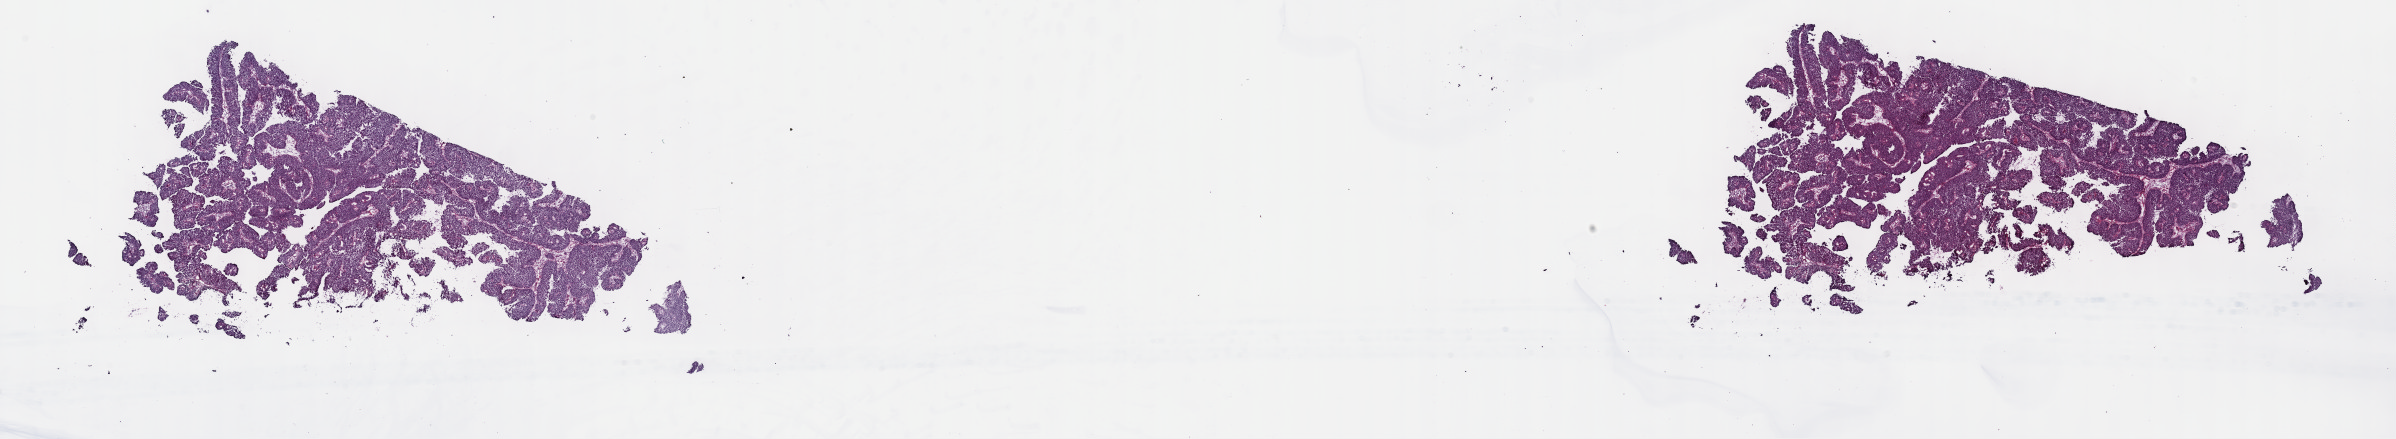
H&E-stained whole-slide image — whole scanned area (about 38.8 x 7.1 mm) shown as a low-resolution overview, frozen section from the top of the tissue portion, bladder, primary tumour sample. Patient: female, age at initial diagnosis 50 years. Histologic grade: high grade. Composition of this section per pathologist review: tumour cells 100%, tumour nuclei 80%, normal cells 0%, stromal cells 0%, necrosis 0%. Inflammatory infiltration, as recorded: lymphocyte infiltration 2%, monocyte infiltration 0%, neutrophil infiltration 0%.
• AJCC pathologic stage: II (6th edition)
• histologic diagnosis: Papillary transitional cell carcinoma
• TNM: T2b N0 MX